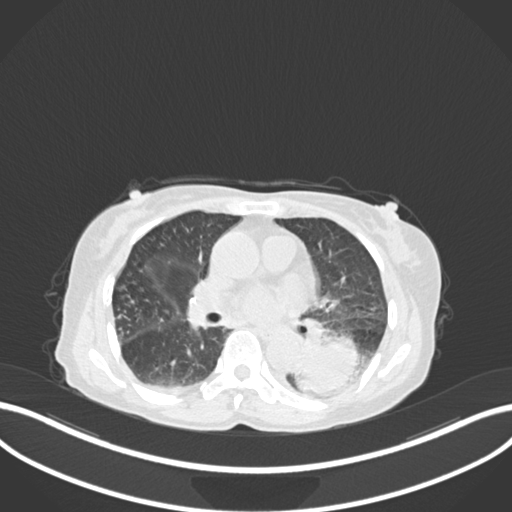
Chest CT, one axial slice; position 86 of 233 along the scan axis; reconstruction kernel B30f; lung window (W 1500 / L -600 HU); 512 × 512 image matrix. Female patient, age 78 years. From the clinical record (not read from this slice): clinical TNM (as recorded): T3 N0 M1.
Structures marked on this image (rectangle marked by the reading radiologist):
- lung tumour (recorded histology: squamous cell carcinoma): box from (x=294, y=334) to (x=370, y=400) px